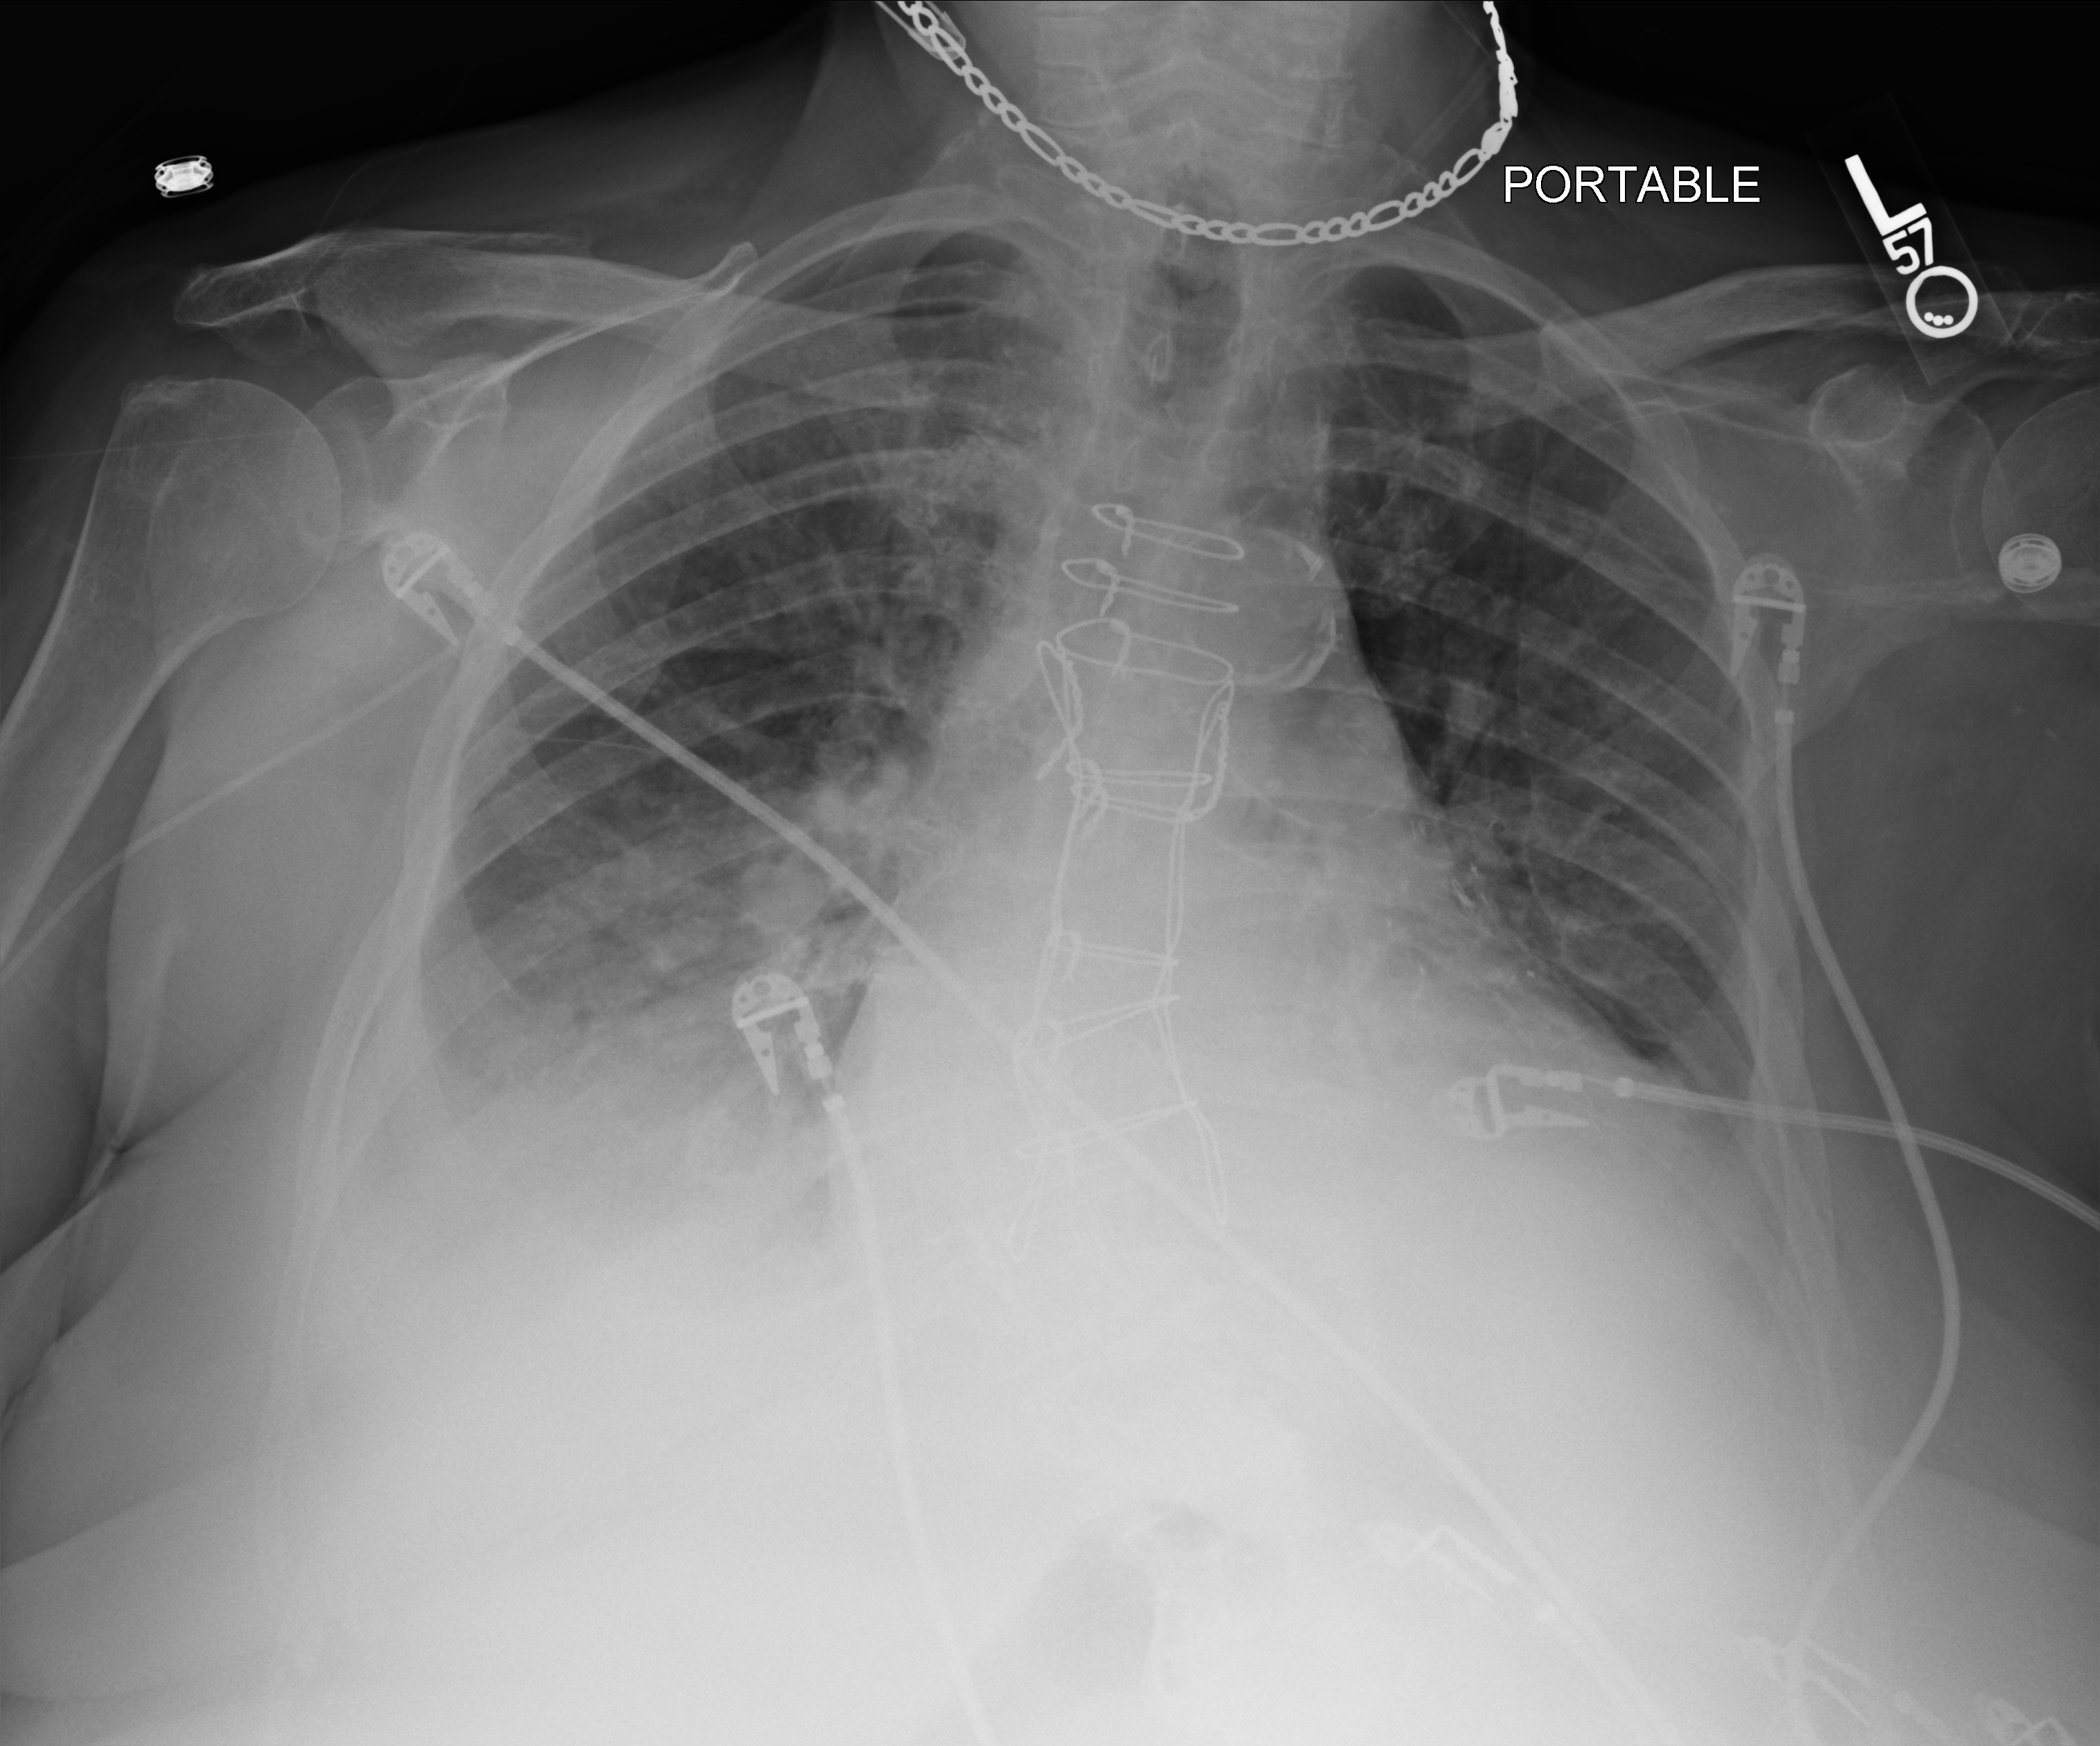
Portable chest radiograph, anteroposterior (AP) projection. Female patient hospitalised with COVID-19, age 75–90 years.
Admission-level facts for this patient (not findings on this image; timing relative to this image not recorded): admitted to intensive care during this hospital stay: no.